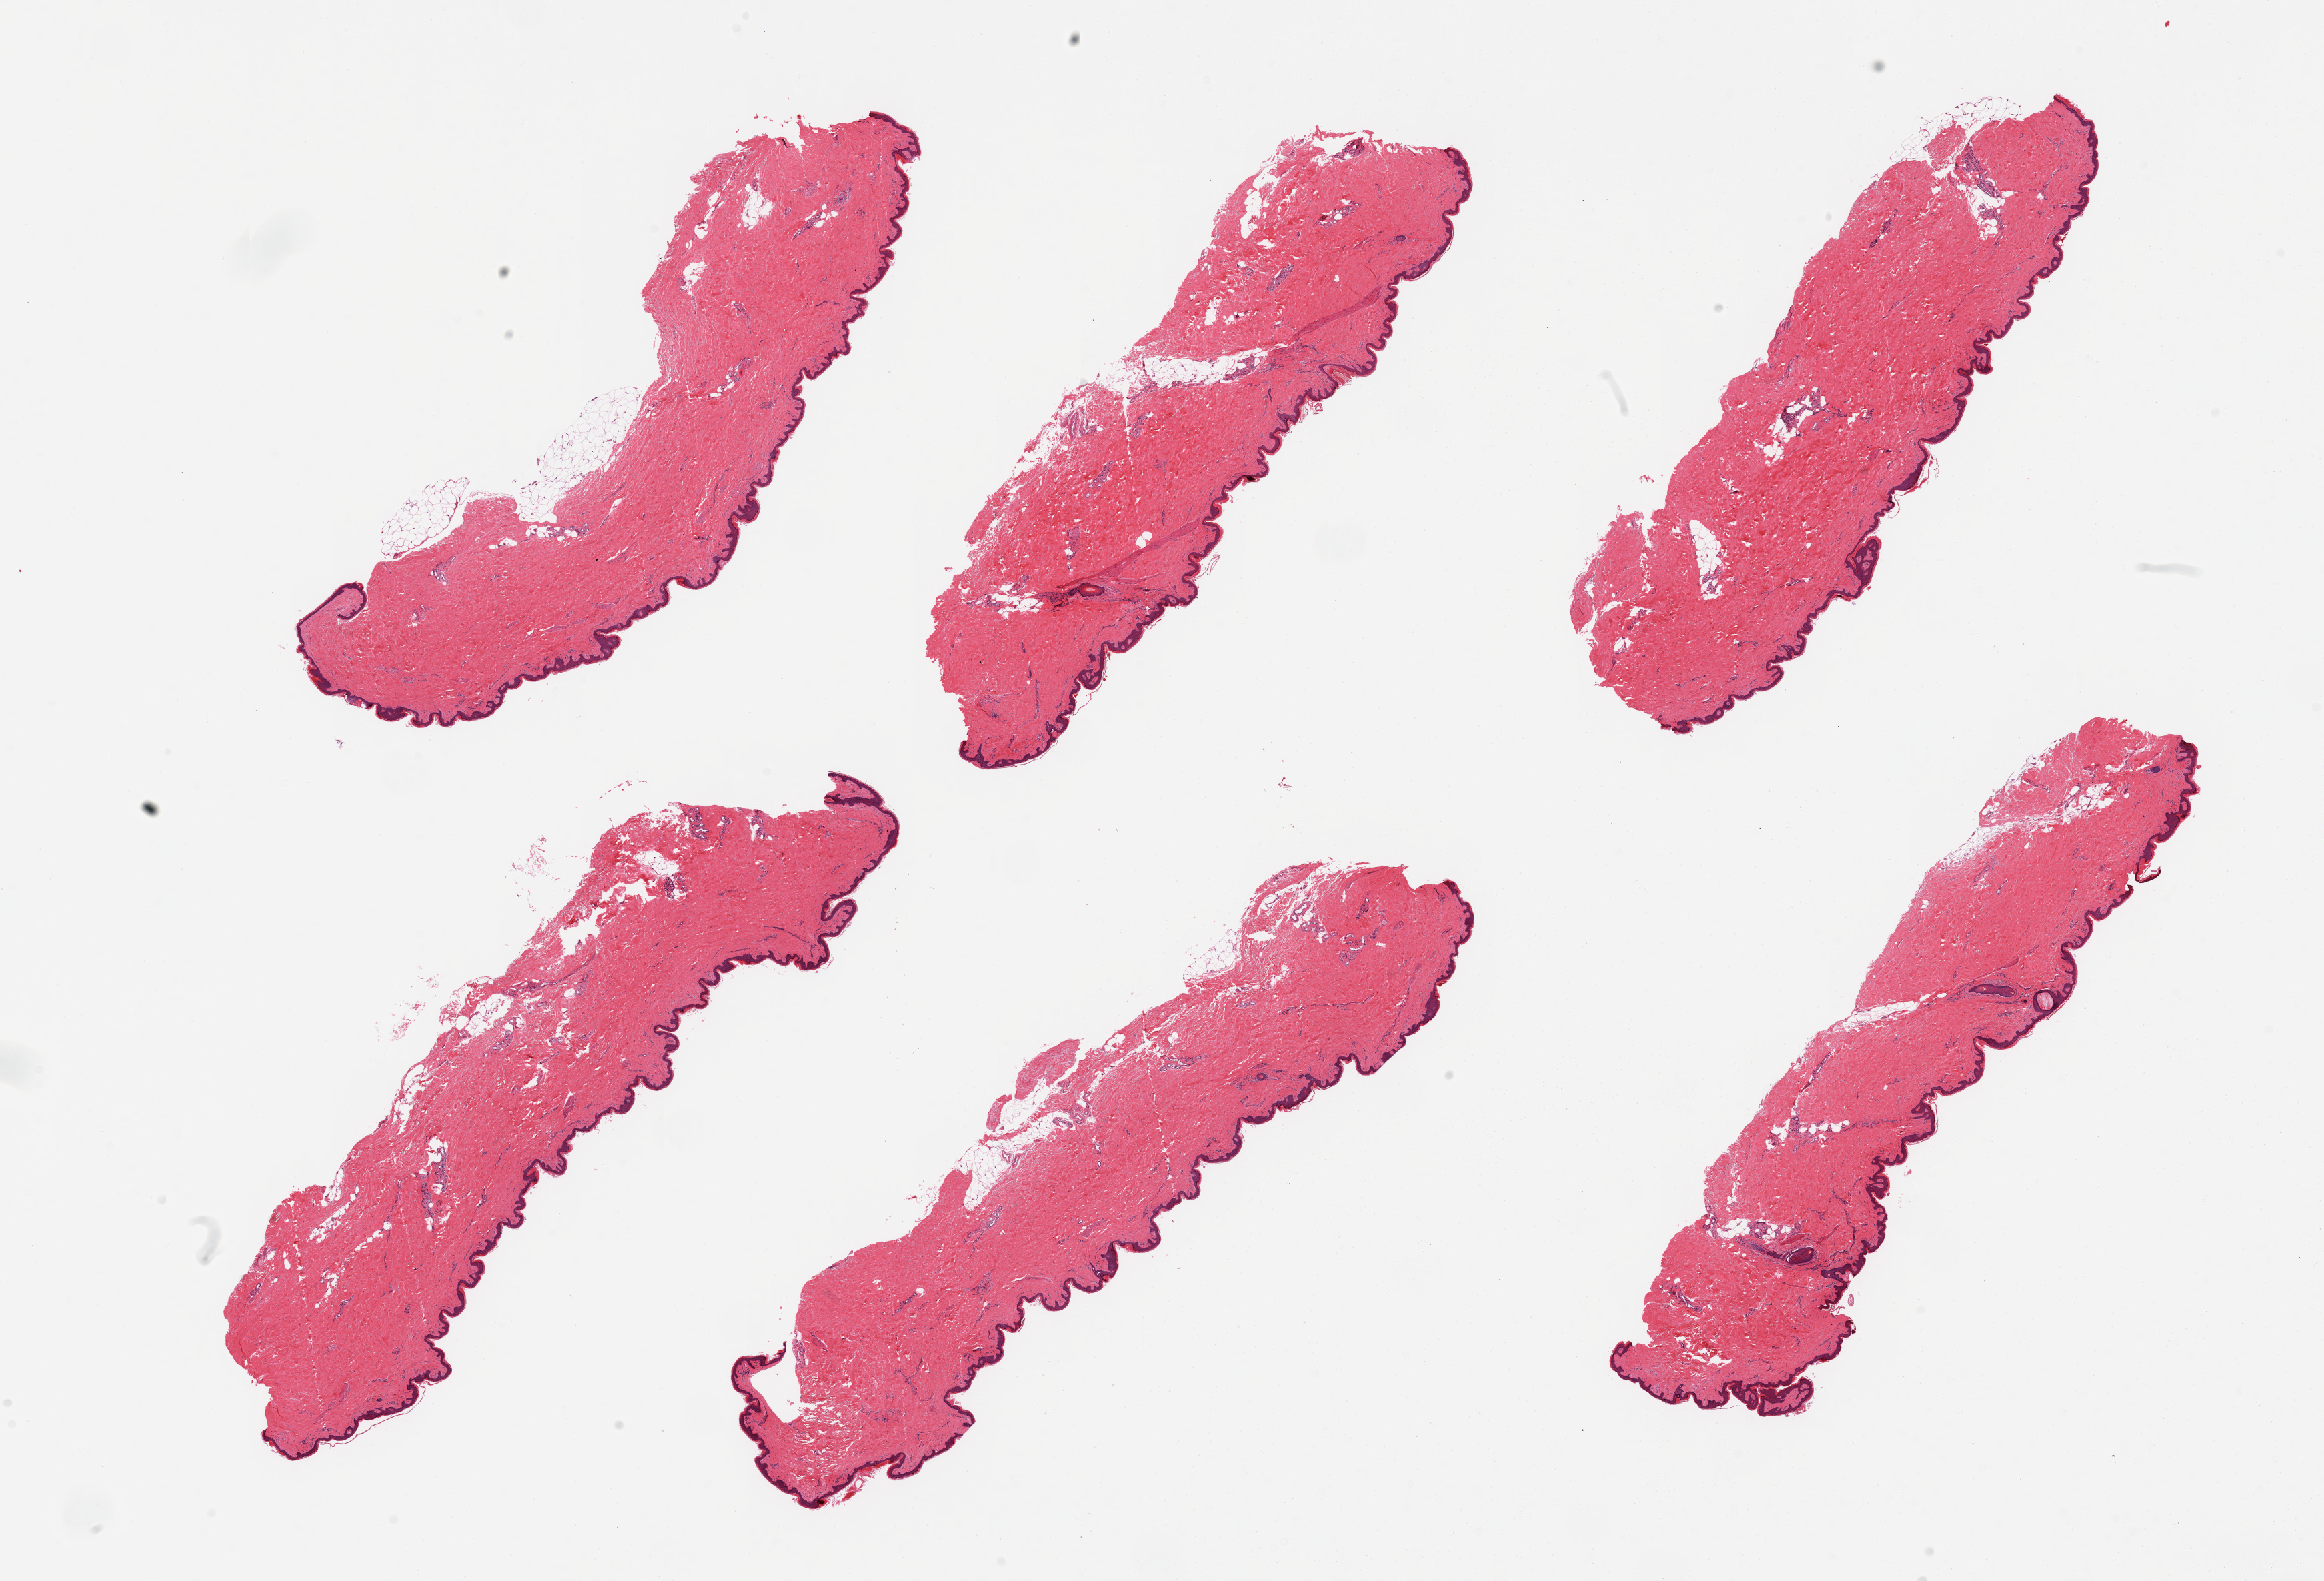
Whole-slide image, H&E stain — shown as a low-resolution overview of the whole scanned area (about 27.6 x 18.8 mm, slide scanned at 20x); PAXgene-fixed paraffin-embedded (PFPE) section; section of skin of lower leg (target tissue); donor tissue sample. Male donor.
• pathologist's review note for this sample: 6 pieces, minimal fat, sqaumous epithelium is ~50-60 microns